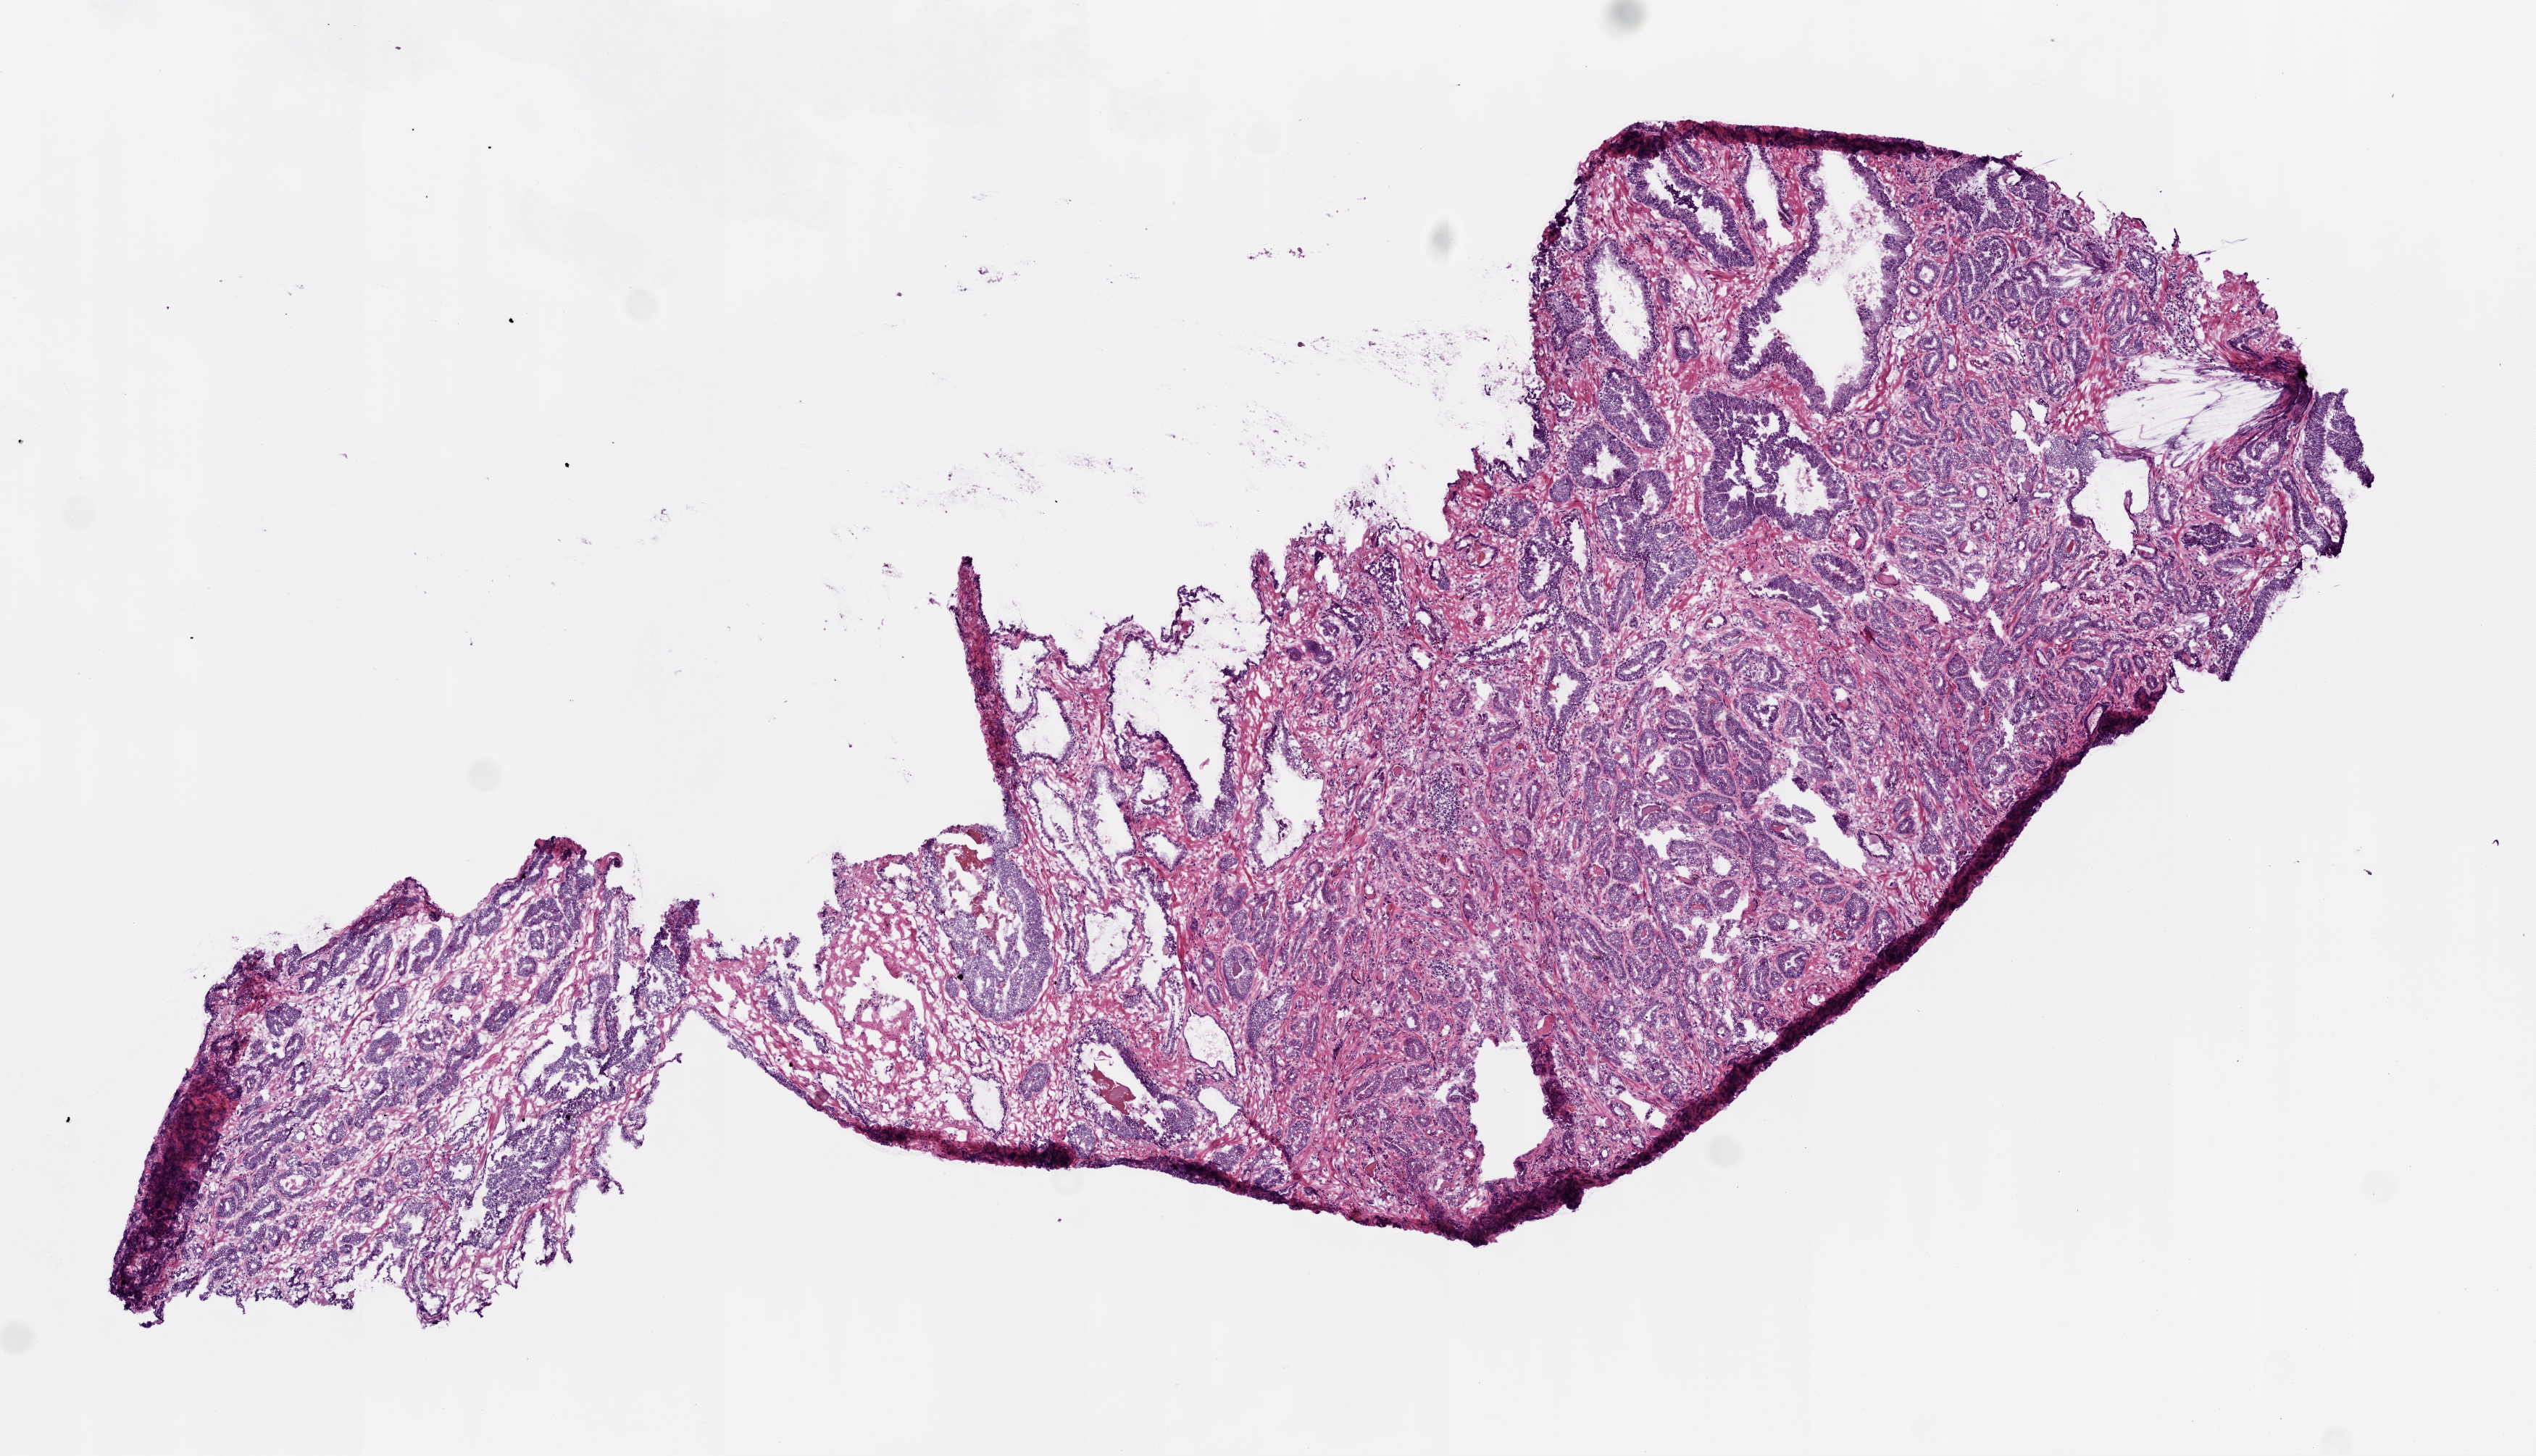
Whole-slide histology image, Hematoxylin and eosin (H&E) stained, whole scanned area (about 7.0 x 4.0 mm, acquisition: 20x scan) shown as a low-resolution overview; frozen section from the top of the tissue portion; prostate, primary tumour sample. Male, age 72 years at initial diagnosis. Slide review estimates, as recorded: tumour cells 70%, tumour nuclei 75%.
Pathologic diagnosis: Acinar cell carcinoma (prostate gland).